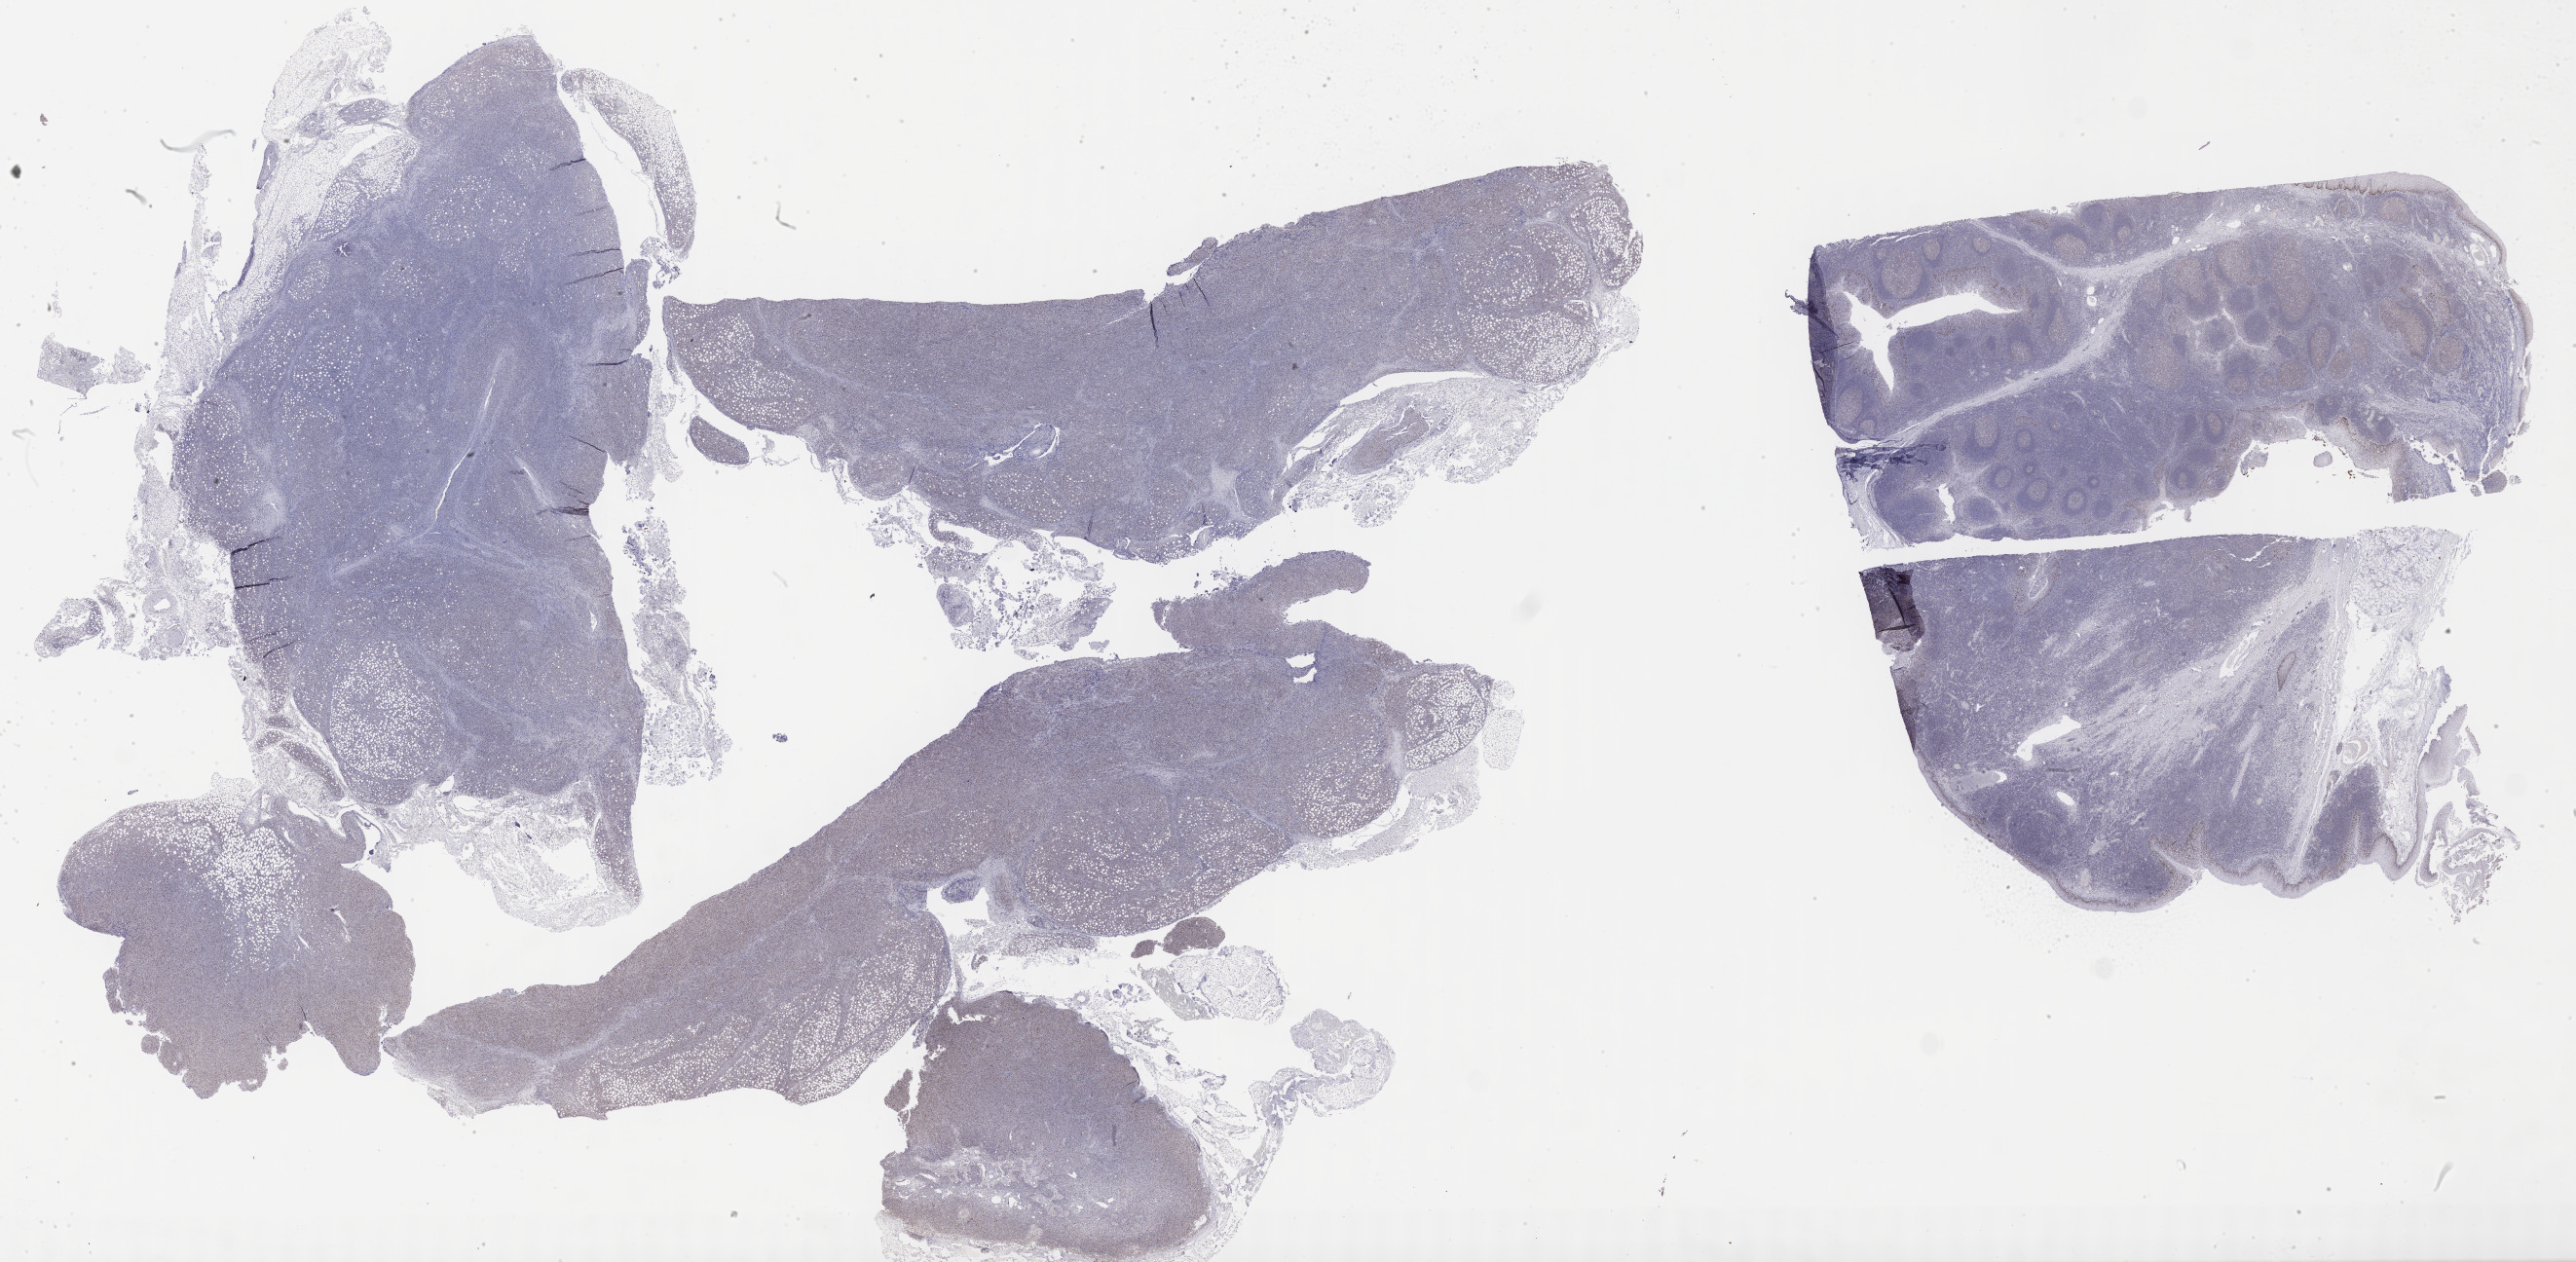
Immunohistochemistry (IHC) whole-slide image stained for p53, shown as a low-resolution overview of the whole scanned area (about 42.8 x 21.0 mm), specimen: tumor tissue, anatomic site: lymph node. Patient male; aged 68.
Diagnosis: Diffuse large B-cell lymphoma, NOS.